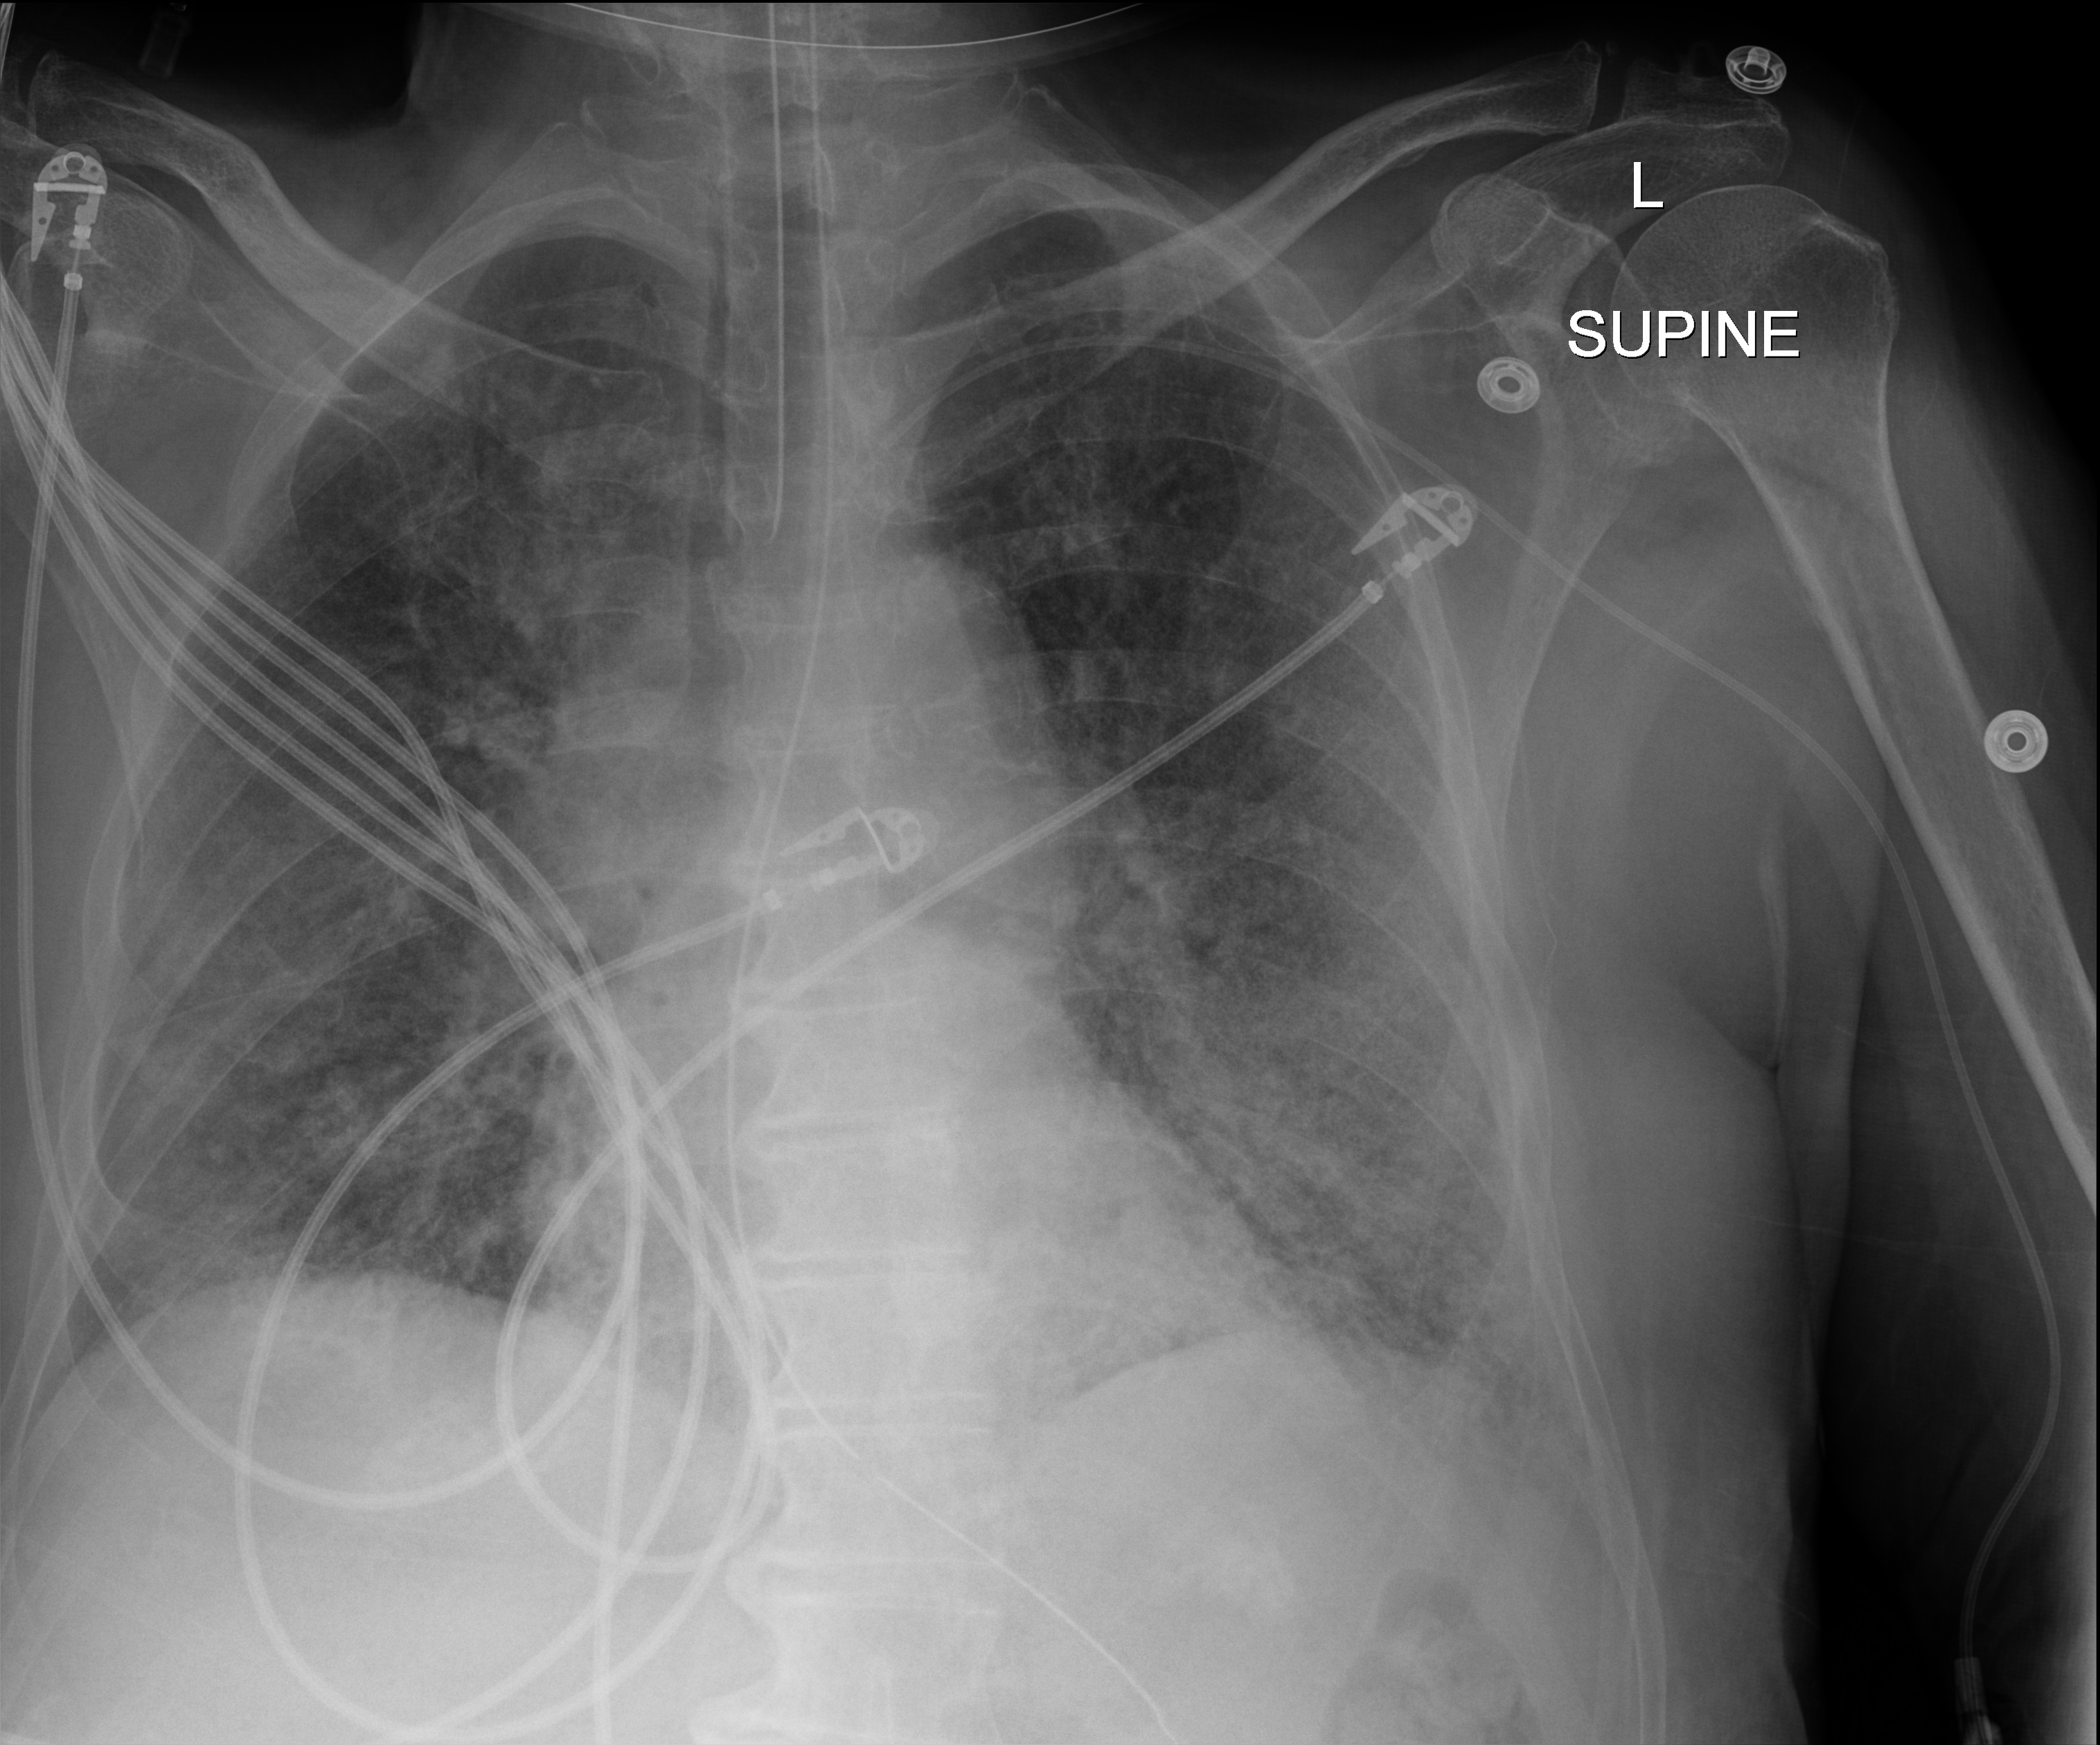
Portable chest radiograph, anteroposterior (AP) projection. Patient hospitalised with COVID-19; male, aged 75–90 years.
Admission-level facts for this patient (not findings on this image; timing relative to this image not recorded): admitted to intensive care during this hospital stay: yes; diabetes (admission record): no; mechanically ventilated during this hospital stay: yes.